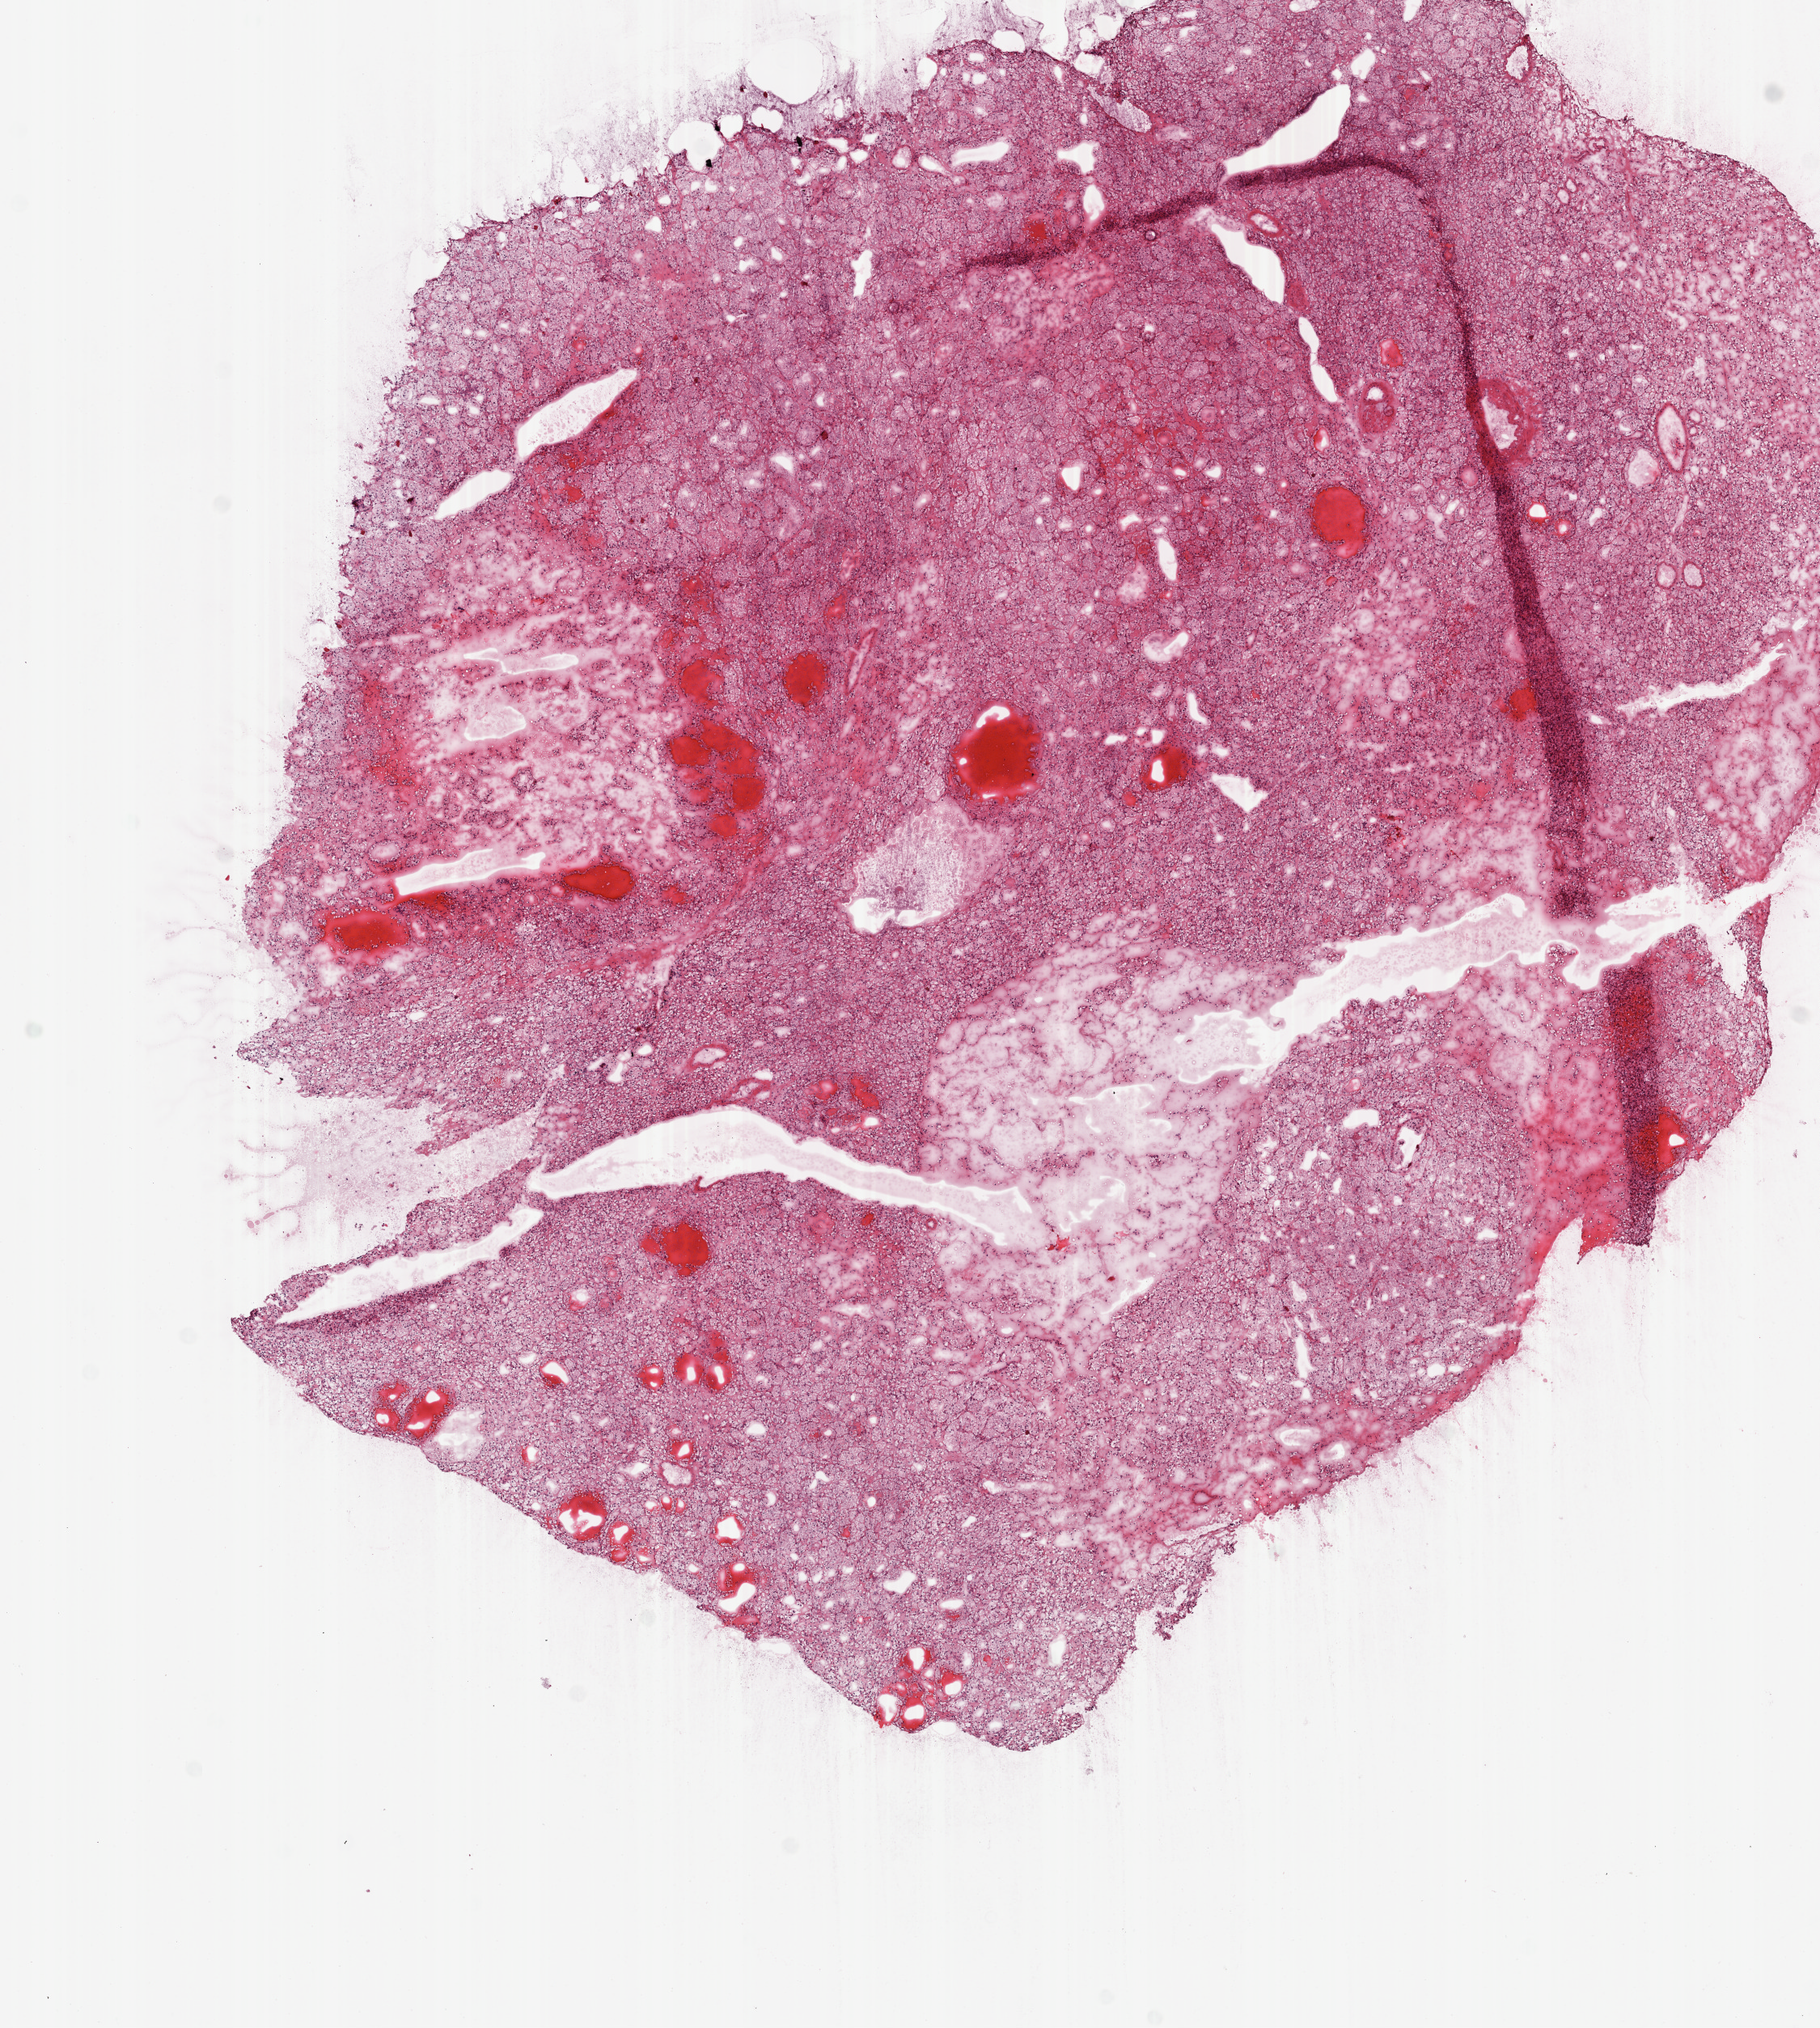
H&E-stained whole-slide image, low-resolution overview of the scanned area, about 9.0 x 10.1 mm. Frozen section. Kidney, primary tumour sample. Patient: female, age at initial diagnosis 50 years.
Pathologic diagnosis: Clear cell adenocarcinoma, NOS.